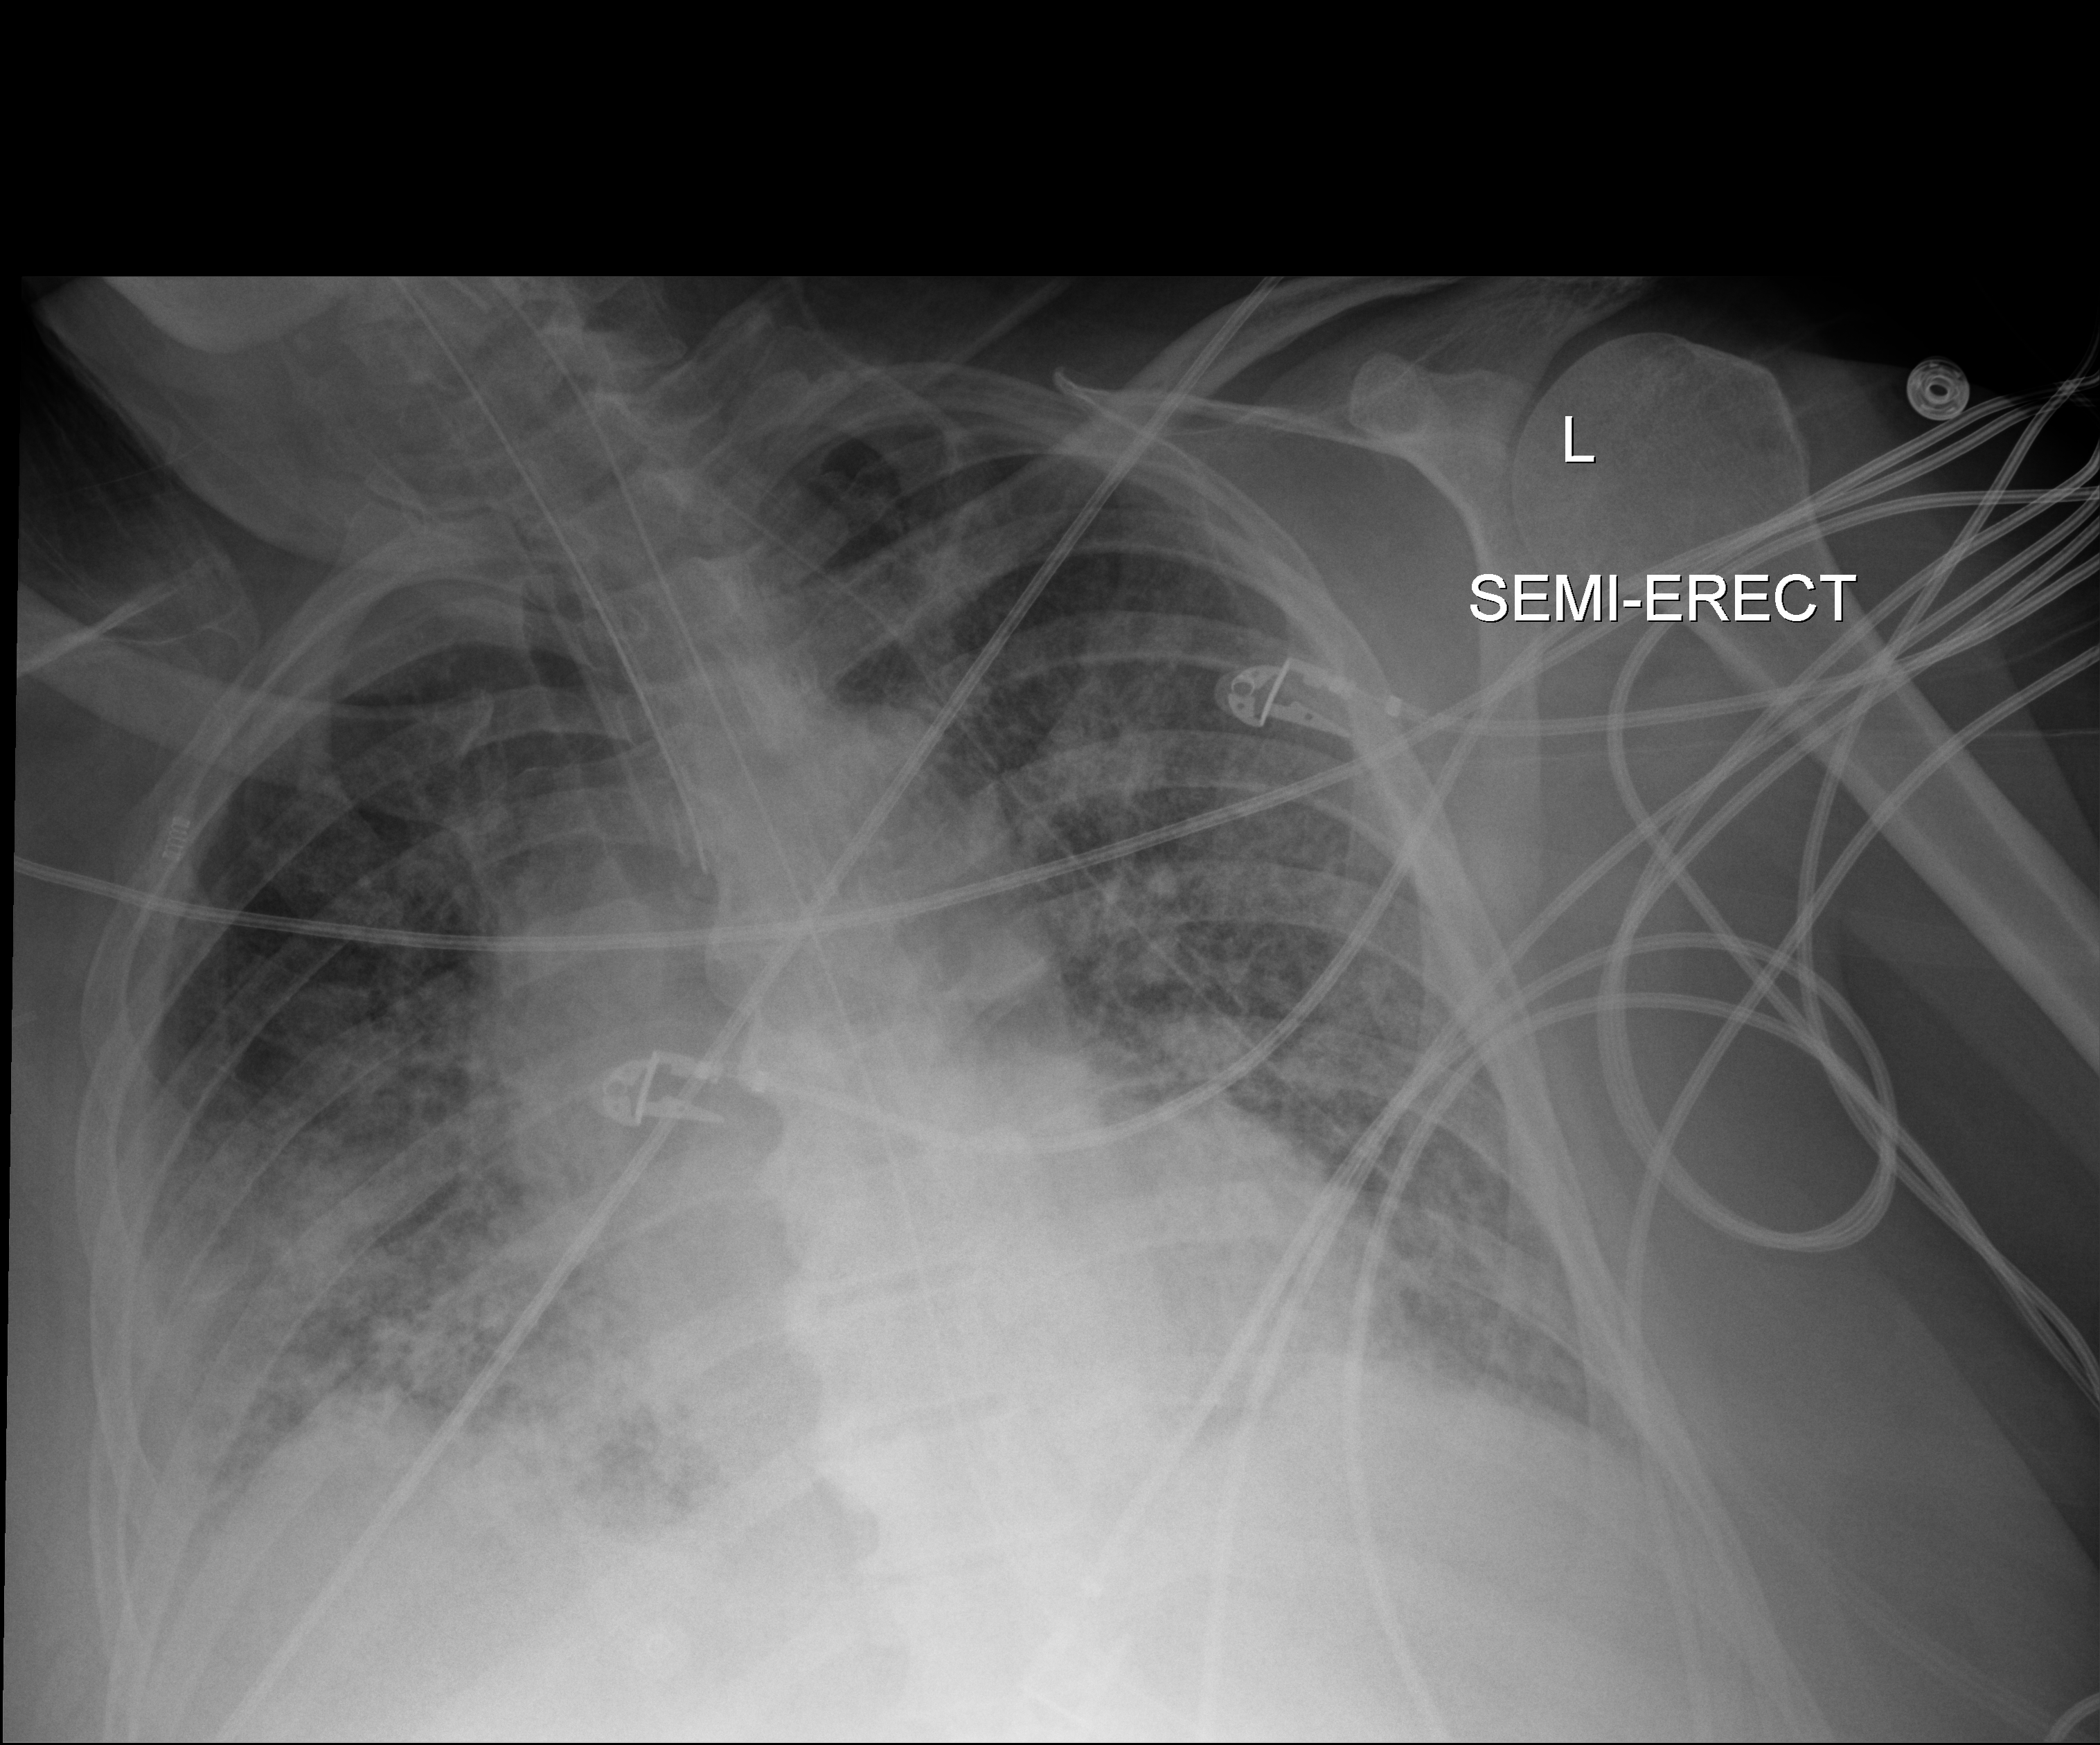
Portable chest radiograph, anteroposterior (AP) projection. Male patient hospitalised with COVID-19, age 60–74 years.
From the hospital-stay record, not from the radiograph (when in the stay this image was taken is not recorded): admitted to intensive care during this hospital stay: yes; hypertension (admission record): yes.